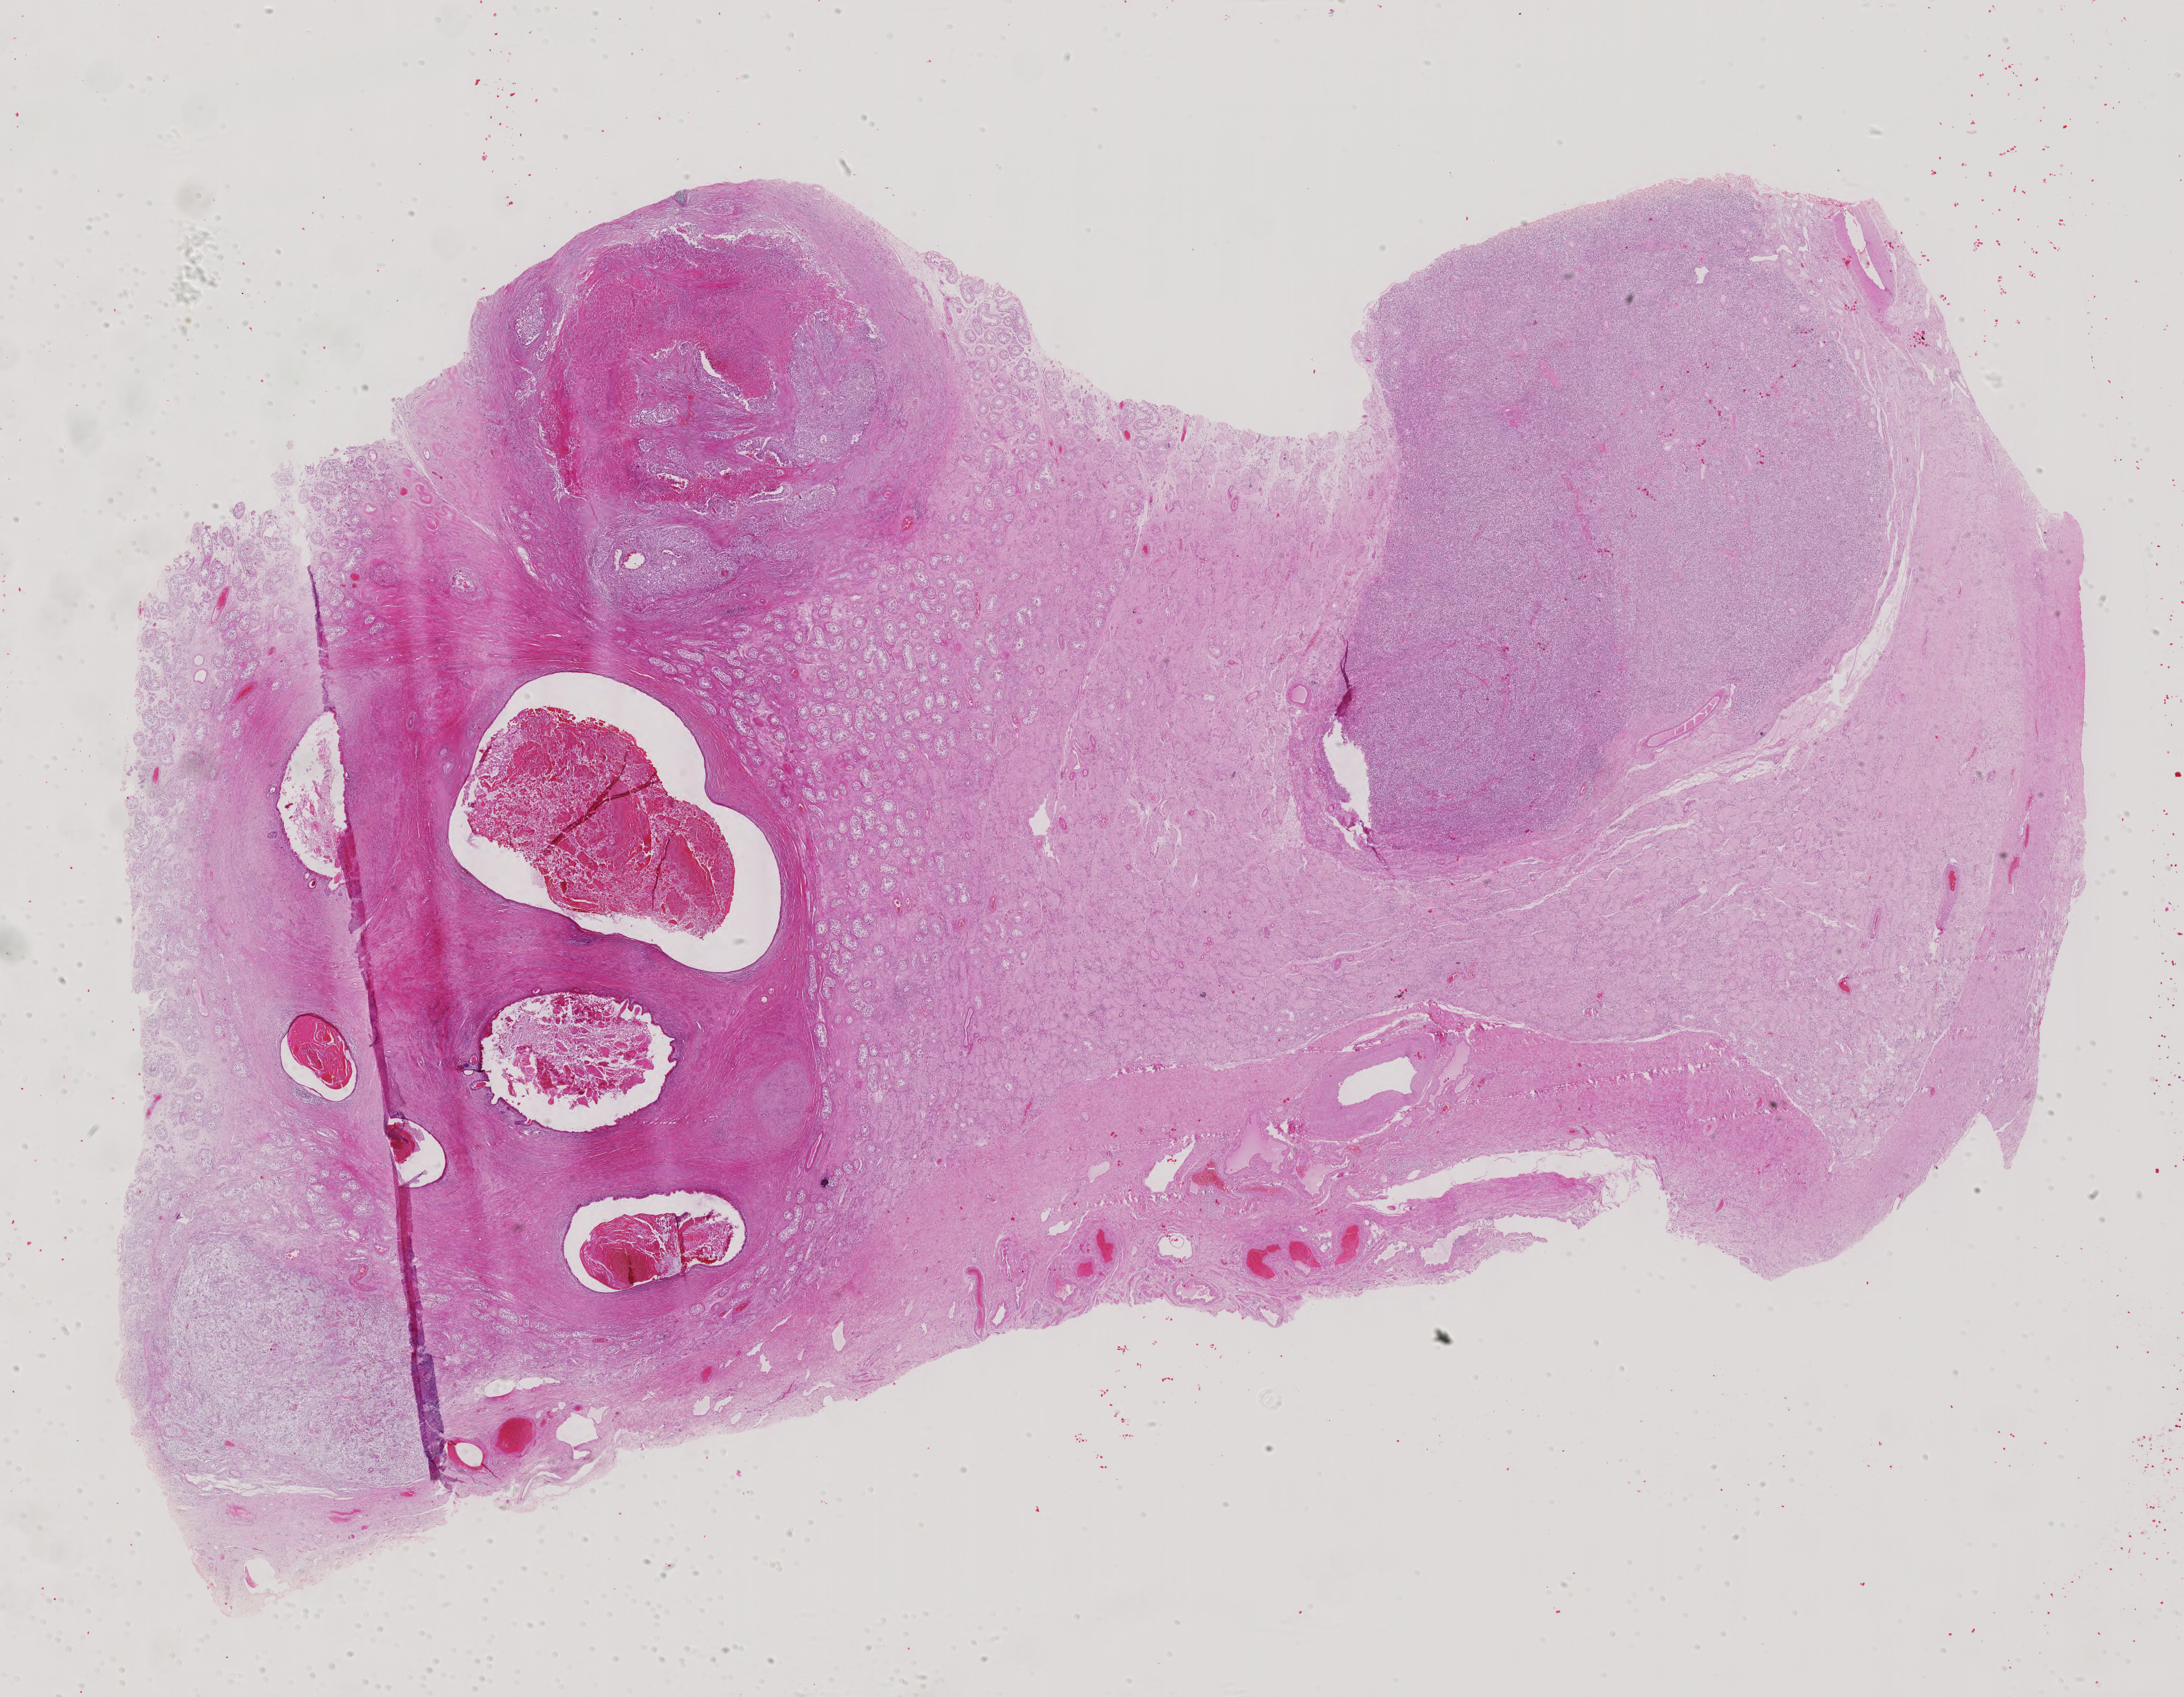
Digitized H&E tissue section (whole slide), shown as a low-resolution overview of the whole scanned area (about 28.0 x 21.7 mm). Formalin-fixed paraffin-embedded (FFPE) diagnostic section. Primary tumour sample from the testis. Patient: male, age at initial diagnosis 27 years.
Diagnosis: Embryonal carcinoma, NOS. AJCC pathologic stage: IIIA (5th edition).